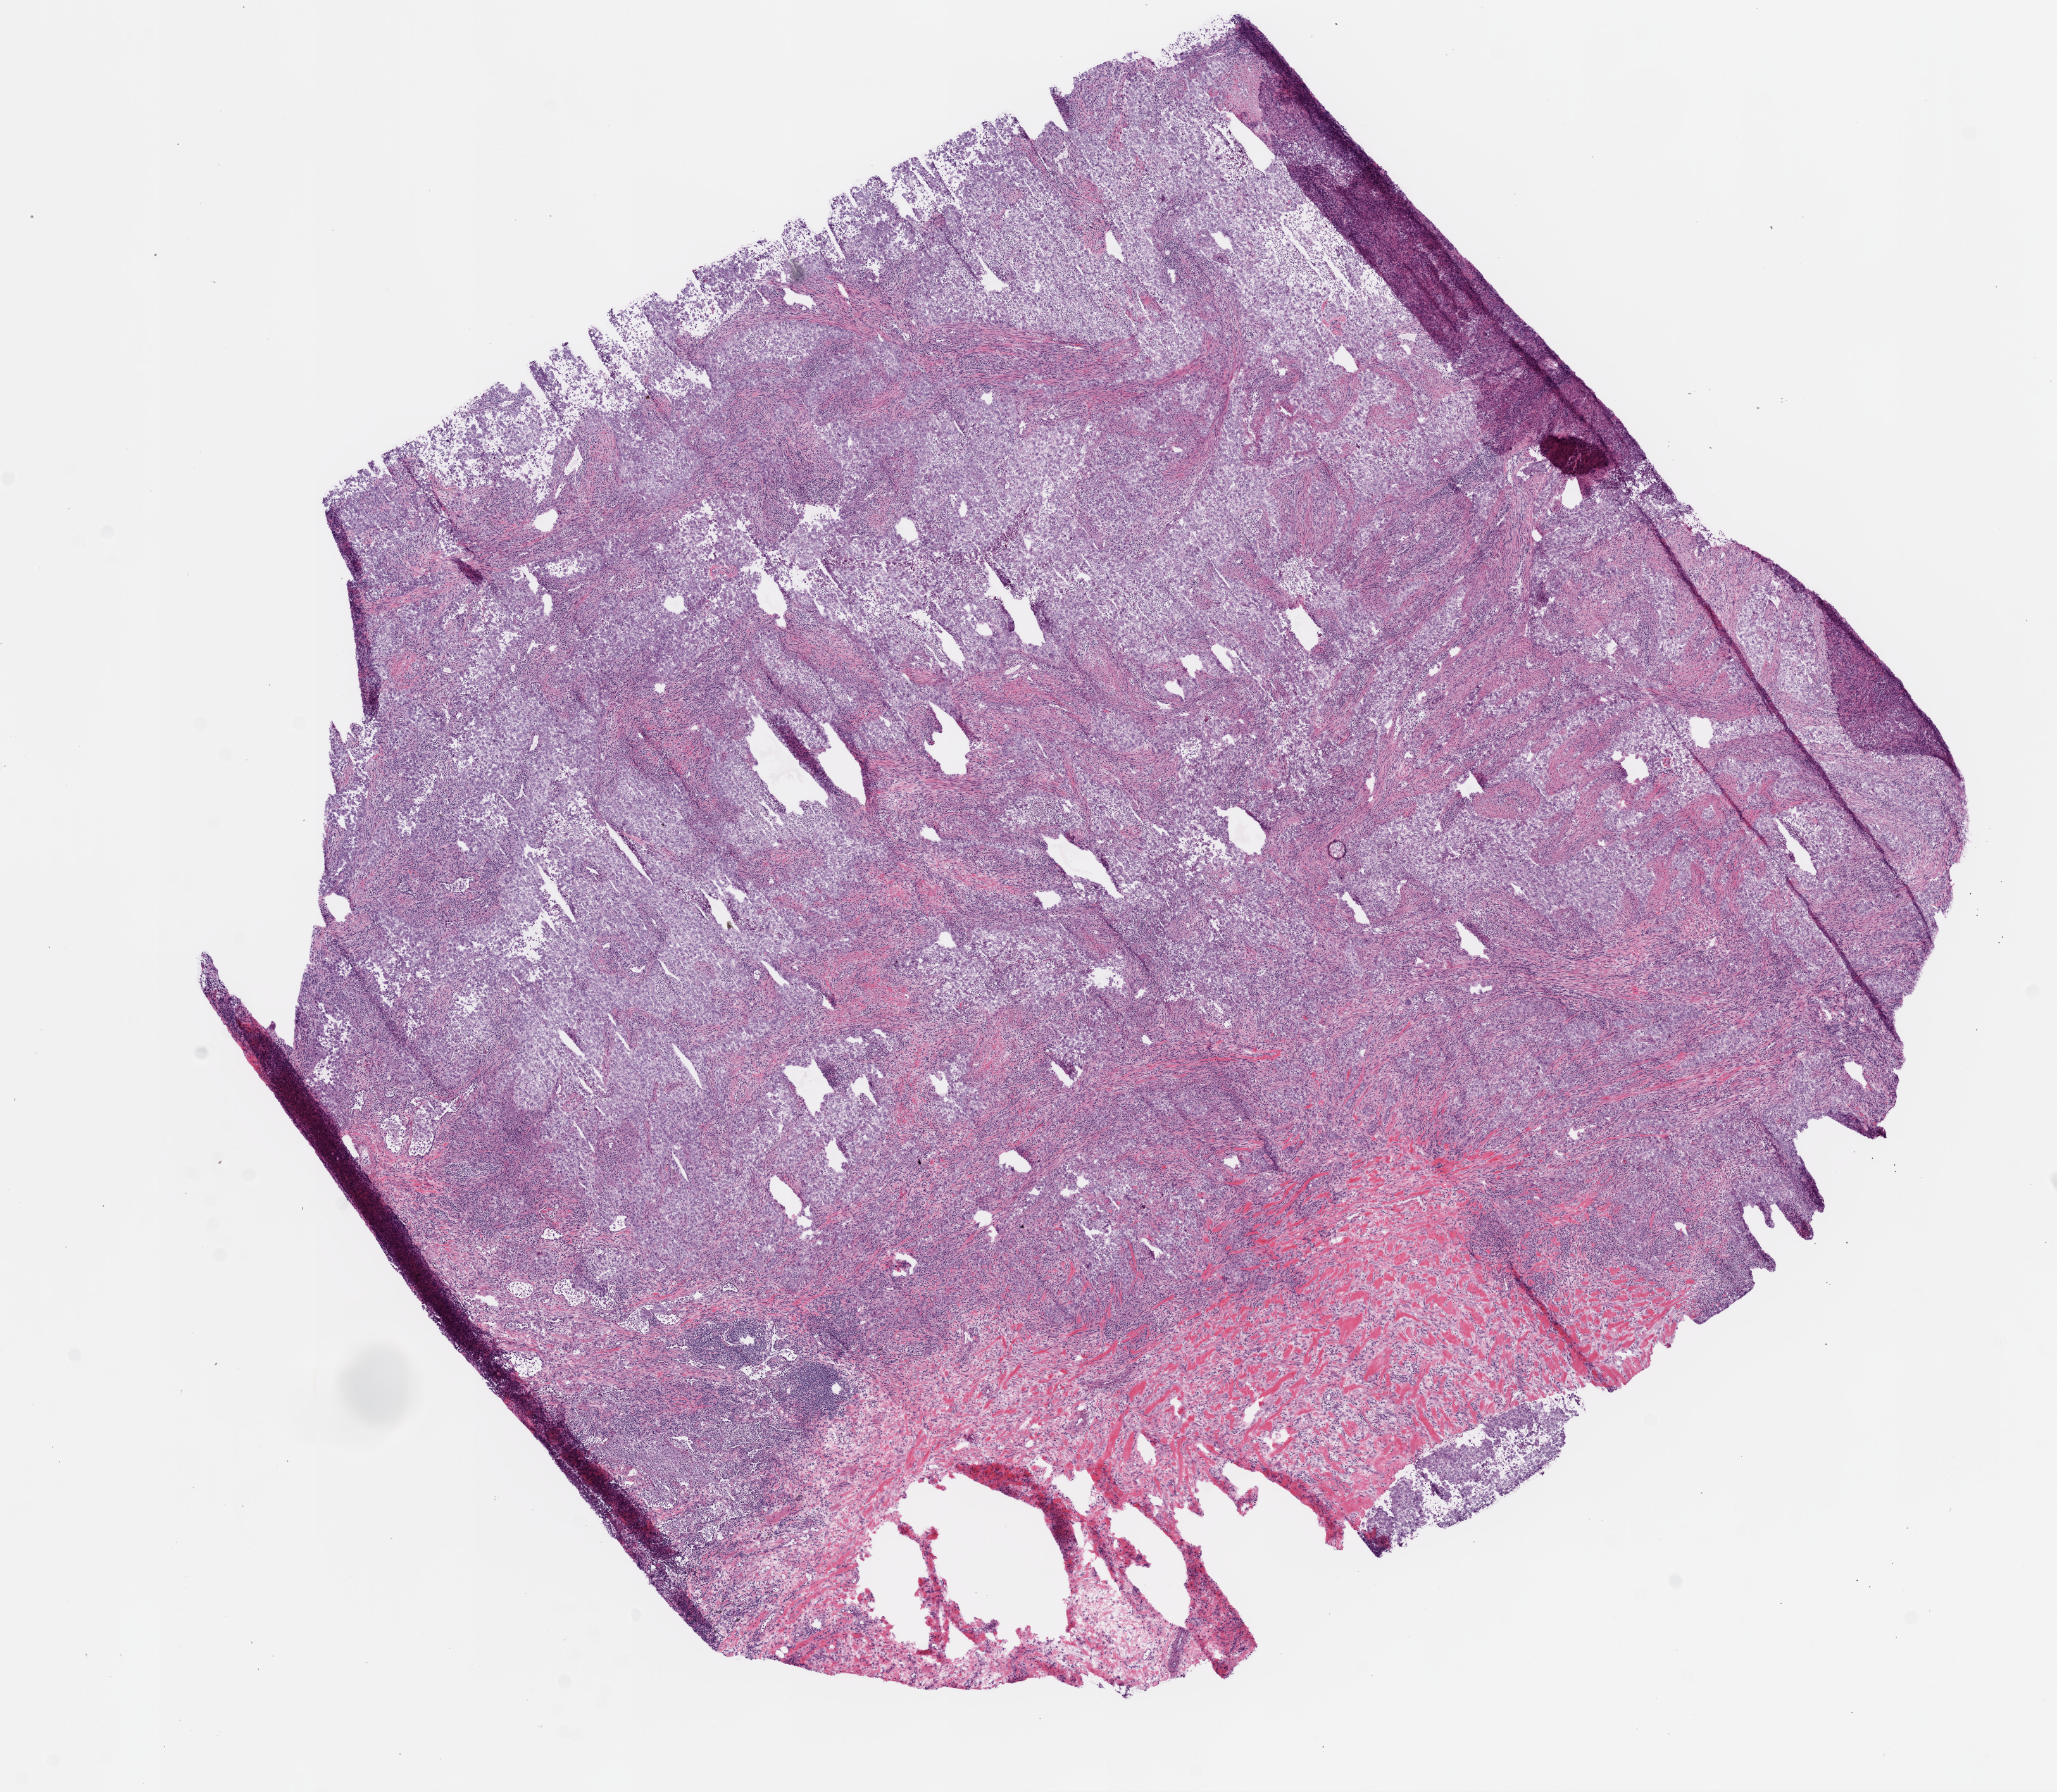
Digitized Hematoxylin and eosin (H&E) stained tissue section (whole slide) — low-resolution overview of the scanned area, about 13.0 x 11.4 mm (acquisition: 20x scan). Frozen section from the bottom of the tissue portion. Primary tumour sample from the lung. Patient: male, age at initial diagnosis 51 years. Composition of this section per pathologist review: tumour cells 80%, tumour nuclei 85%, normal cells 0%, stromal cells 20%, necrosis 0%. Infiltration values recorded for this section: lymphocyte infiltration 10%.
* histologic diagnosis: Adenocarcinoma, NOS
* AJCC pathologic stage: IB
* TNM: T2 N0 M0